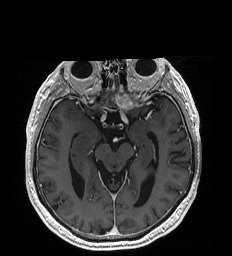
Brain MRI from a brain-tumour surgery series, one axial slice; position 118 of 192 along the scan axis; T1-weighted post-contrast; 232 × 256 image matrix. From the clinical record (not read from this slice): histopathology: Glioblastoma; WHO grade: 4; IDH mutation: no.
Outlined on this slice (manually delineated by an expert):
- tumour: box from (x=116, y=87) to (x=132, y=109) px